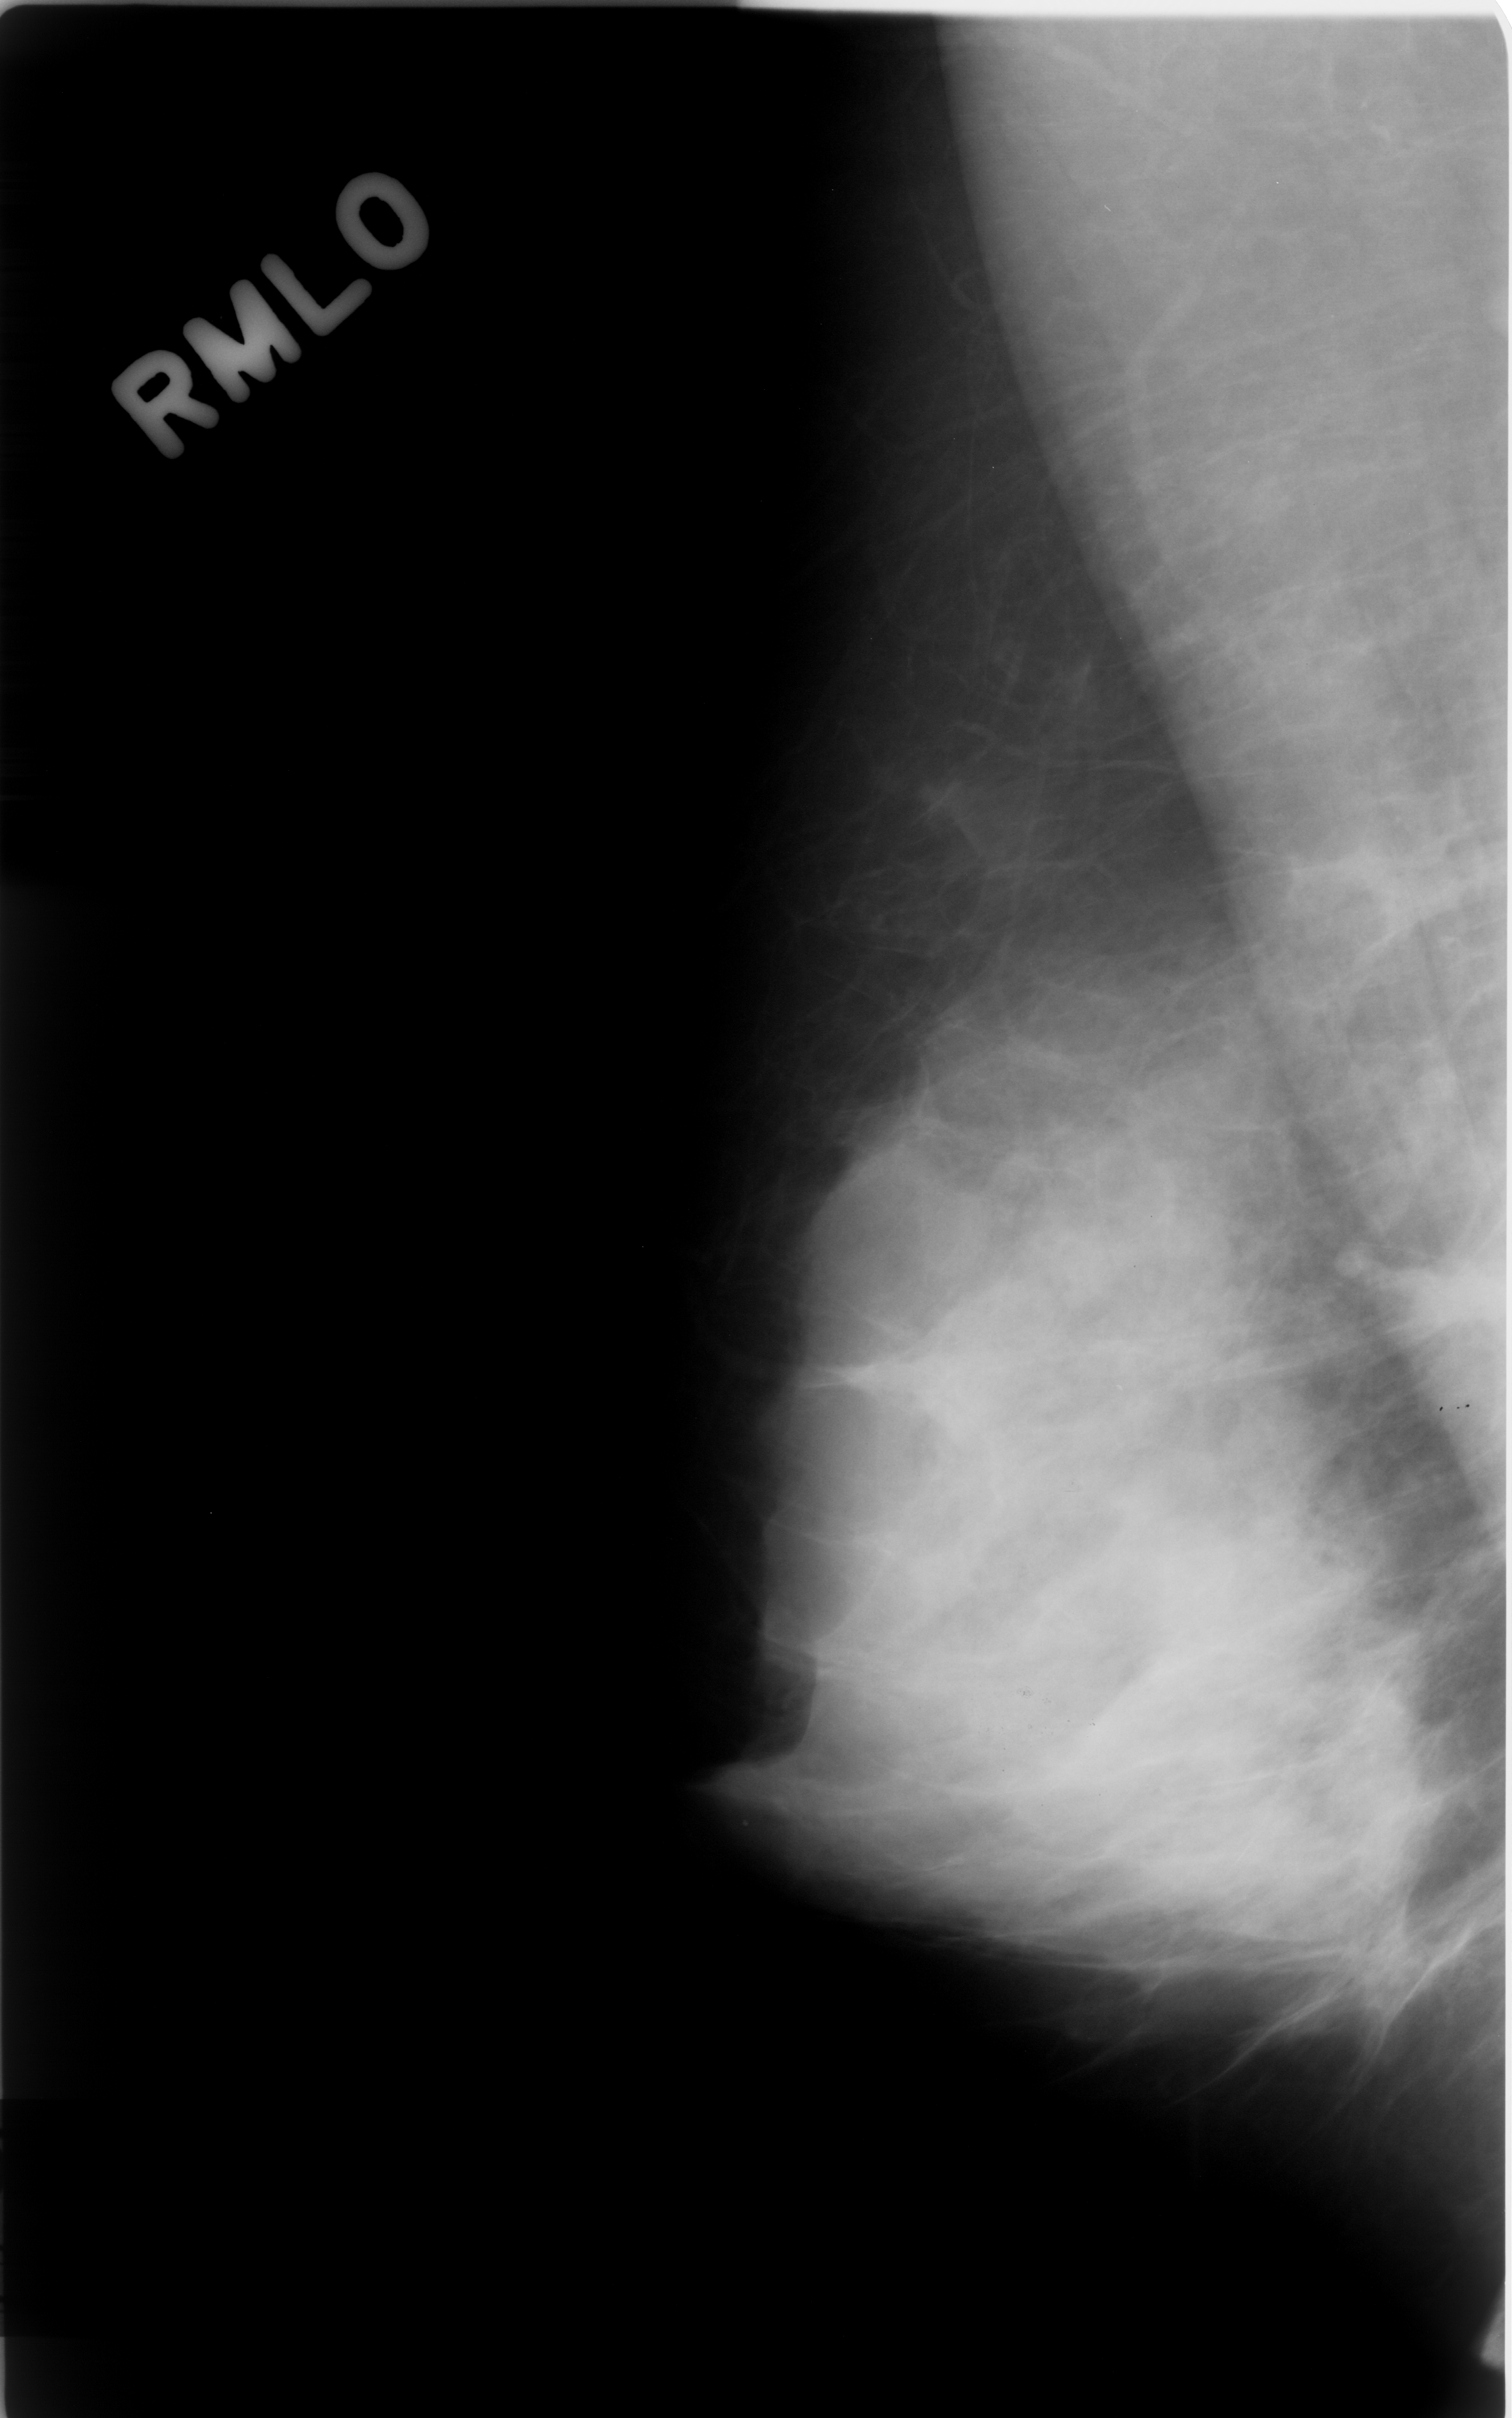
Scanned film-screen mammogram, right breast, mediolateral oblique (MLO) view.
- Finding: mass, shape irregular, margins spiculated; BI-RADS assessment category 4; subtlety rating 5 on a 1 (subtle) to 5 (obvious) scale; benign without callback (not worked up further).